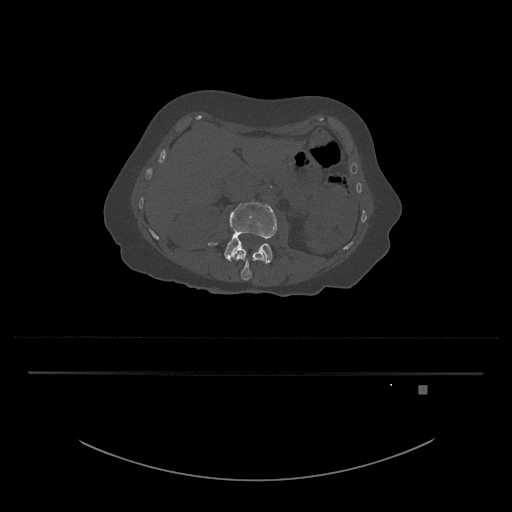
CT including the spine, one axial slice; position 455 of 797 along the scan axis; 120 kVp; bone window (W 1800 / L 400 HU); 0.5 mm slice thickness; 512 × 512 image matrix. Female patient, age 57 years. From the clinical record (not read from this slice): primary cancer: cervical.
Annotated regions visible in this slice (semi-automatic segmentation, software-assisted and operator-edited):
- L3 vertebra: bounding box [x1, y1, x2, y2] px = [208, 201, 278, 264]